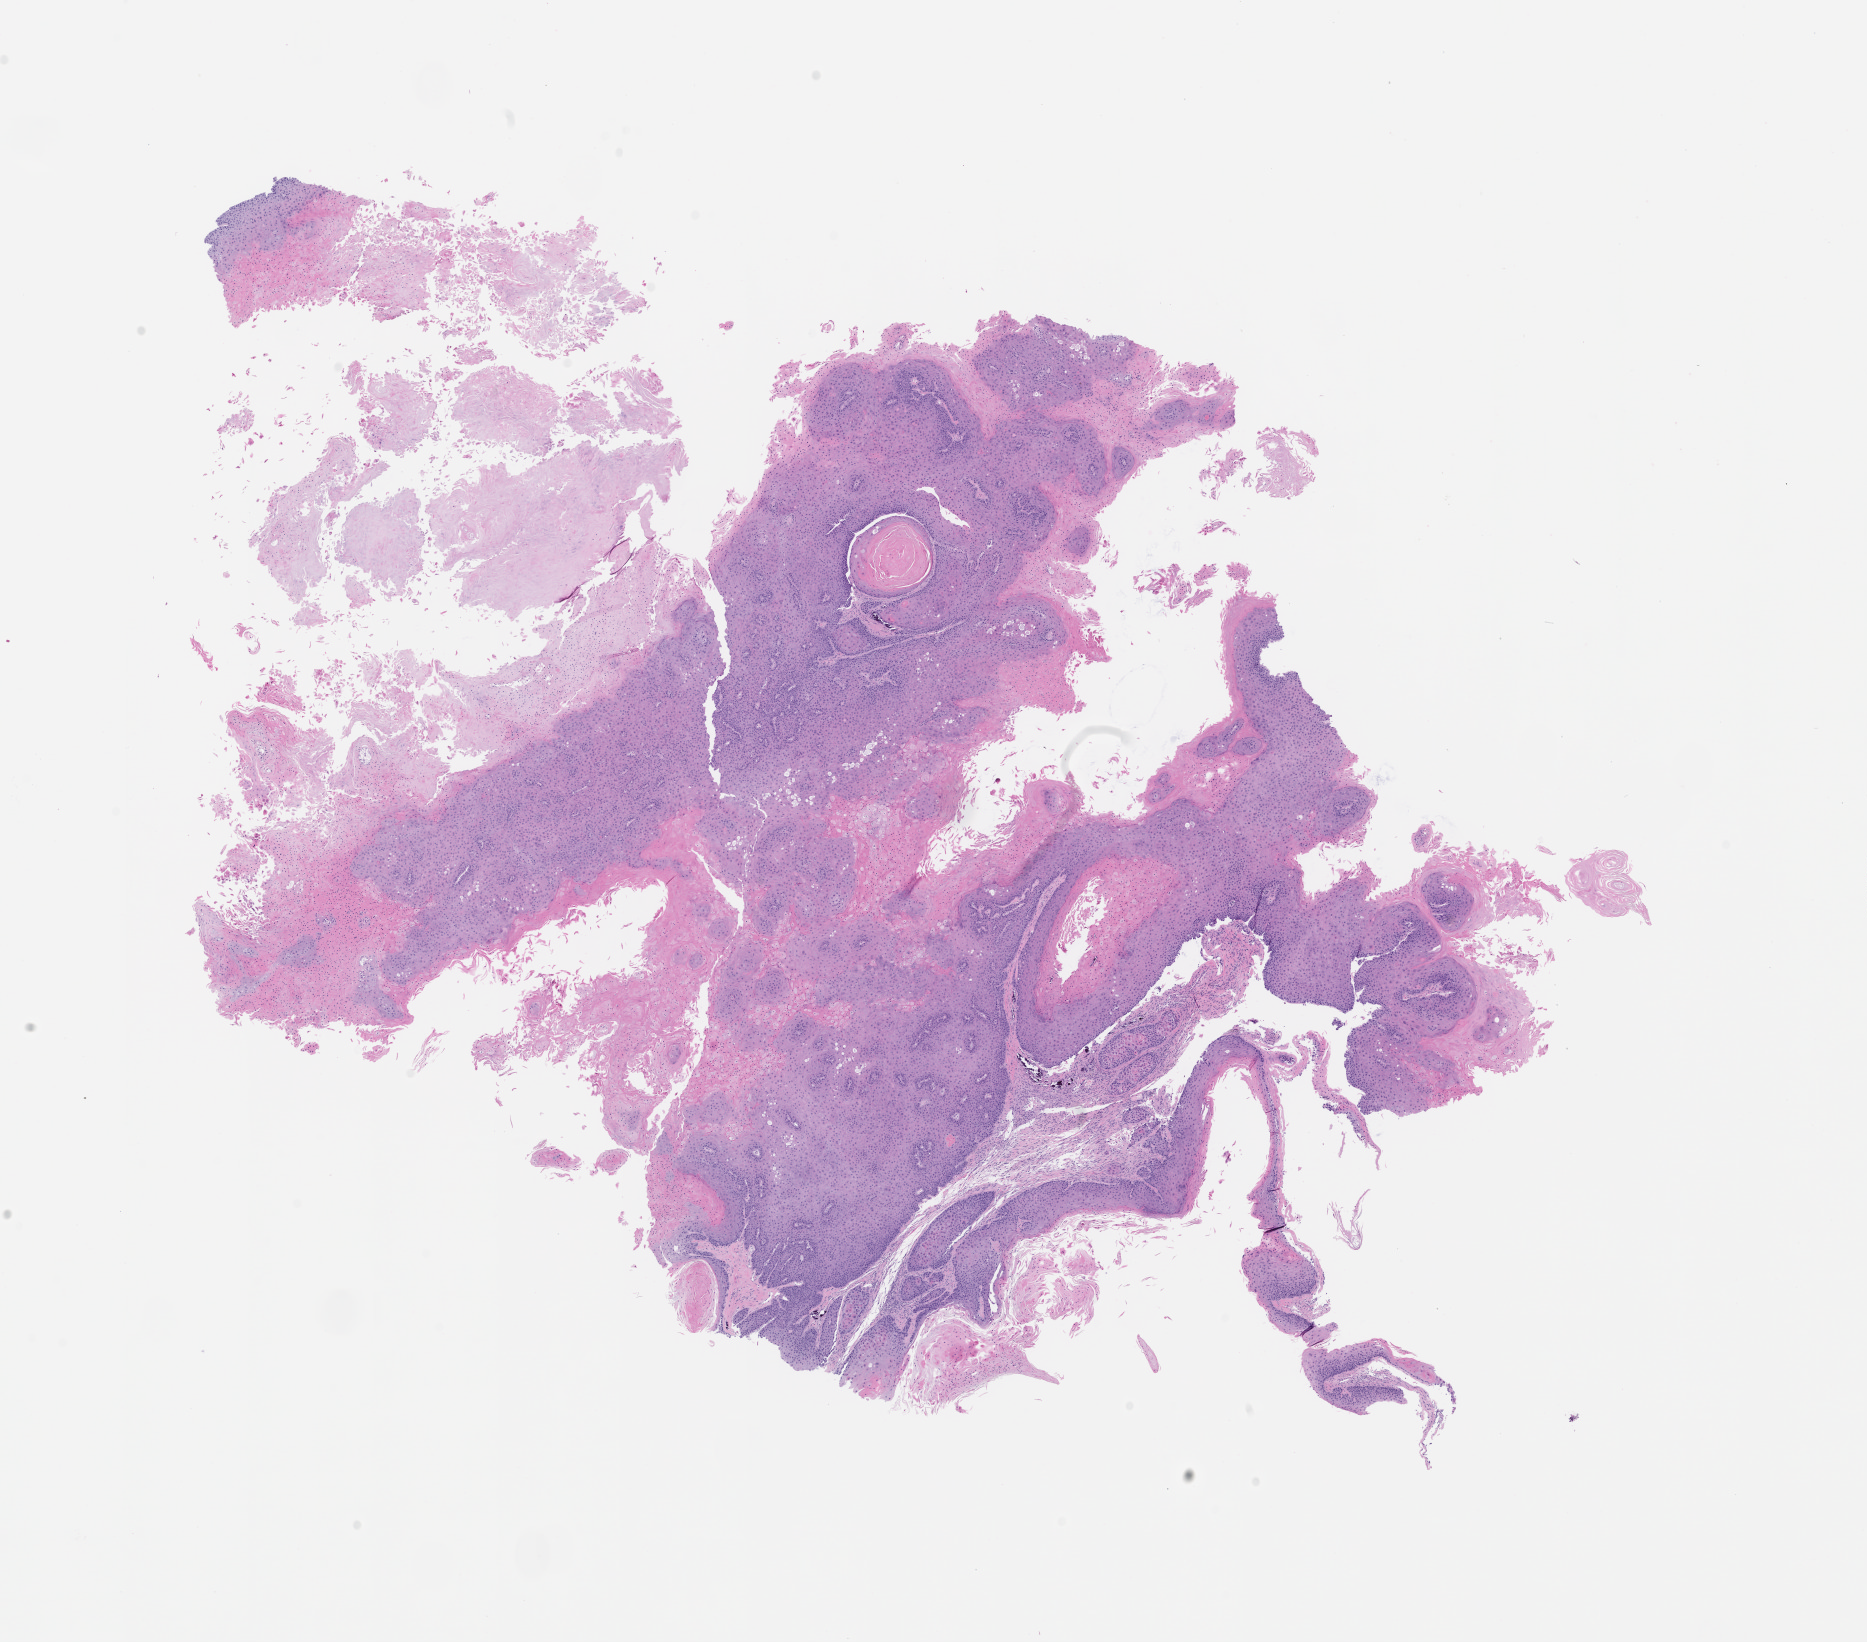
Haematoxylin and eosin whole-slide image of a patient-derived xenograft (PDX) tumor grown in a mouse, passage 1, a low-resolution overview of the entire scanned area, about 15.0 x 13.2 mm, formalin-fixed paraffin-embedded section, originating tumor site category: oral soft tissue.
Originating patient diagnosis: Head and Neck Squamous Cell Carcinoma.